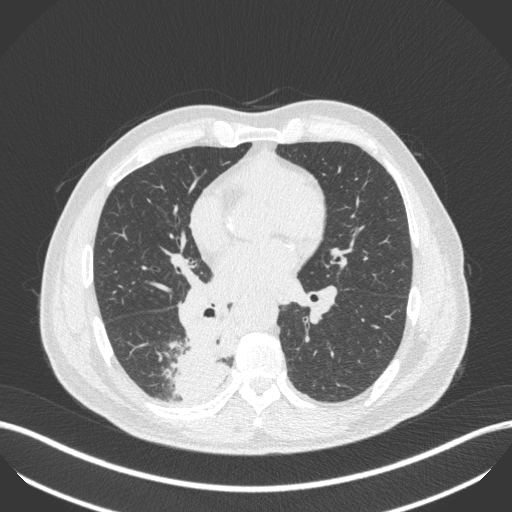
Chest CT, one axial slice. Position 229 of 451 along the scan axis. 100 kVp. Lung window (W 1500 / L -600 HU). 1 mm slice thickness. 512 × 512 image matrix. Male patient, age 61 years. Case-level facts recorded for this patient, not image findings: clinical TNM (as recorded): T1 N0 M0; histopathological grade: G3.
Structures marked on this image (bounding box drawn by a radiologist):
- lung tumour (recorded histology: small cell carcinoma): box from (x=163, y=318) to (x=240, y=405) px